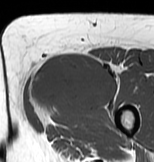
MRI of an extremity soft-tissue mass, one axial slice. Position 32 of 83 along the scan axis. MR volume resampled by the dataset authors to the PET/CT grid (not the native acquisition matrix). 154 × 162 image matrix. Female patient. From the clinical record (not read from this slice): histological type: myxofibrosarcoma; grade: intermediate; site of the primary tumour: left thigh.
Annotated regions visible in this slice (expert contour drawn on MRI and transferred to this co-registered scan by the dataset authors):
- gross tumour volume including surrounding oedema: box from (x=28, y=52) to (x=120, y=128) px
- gross tumour volume (mass): (x=28, y=52)–(x=116, y=113)